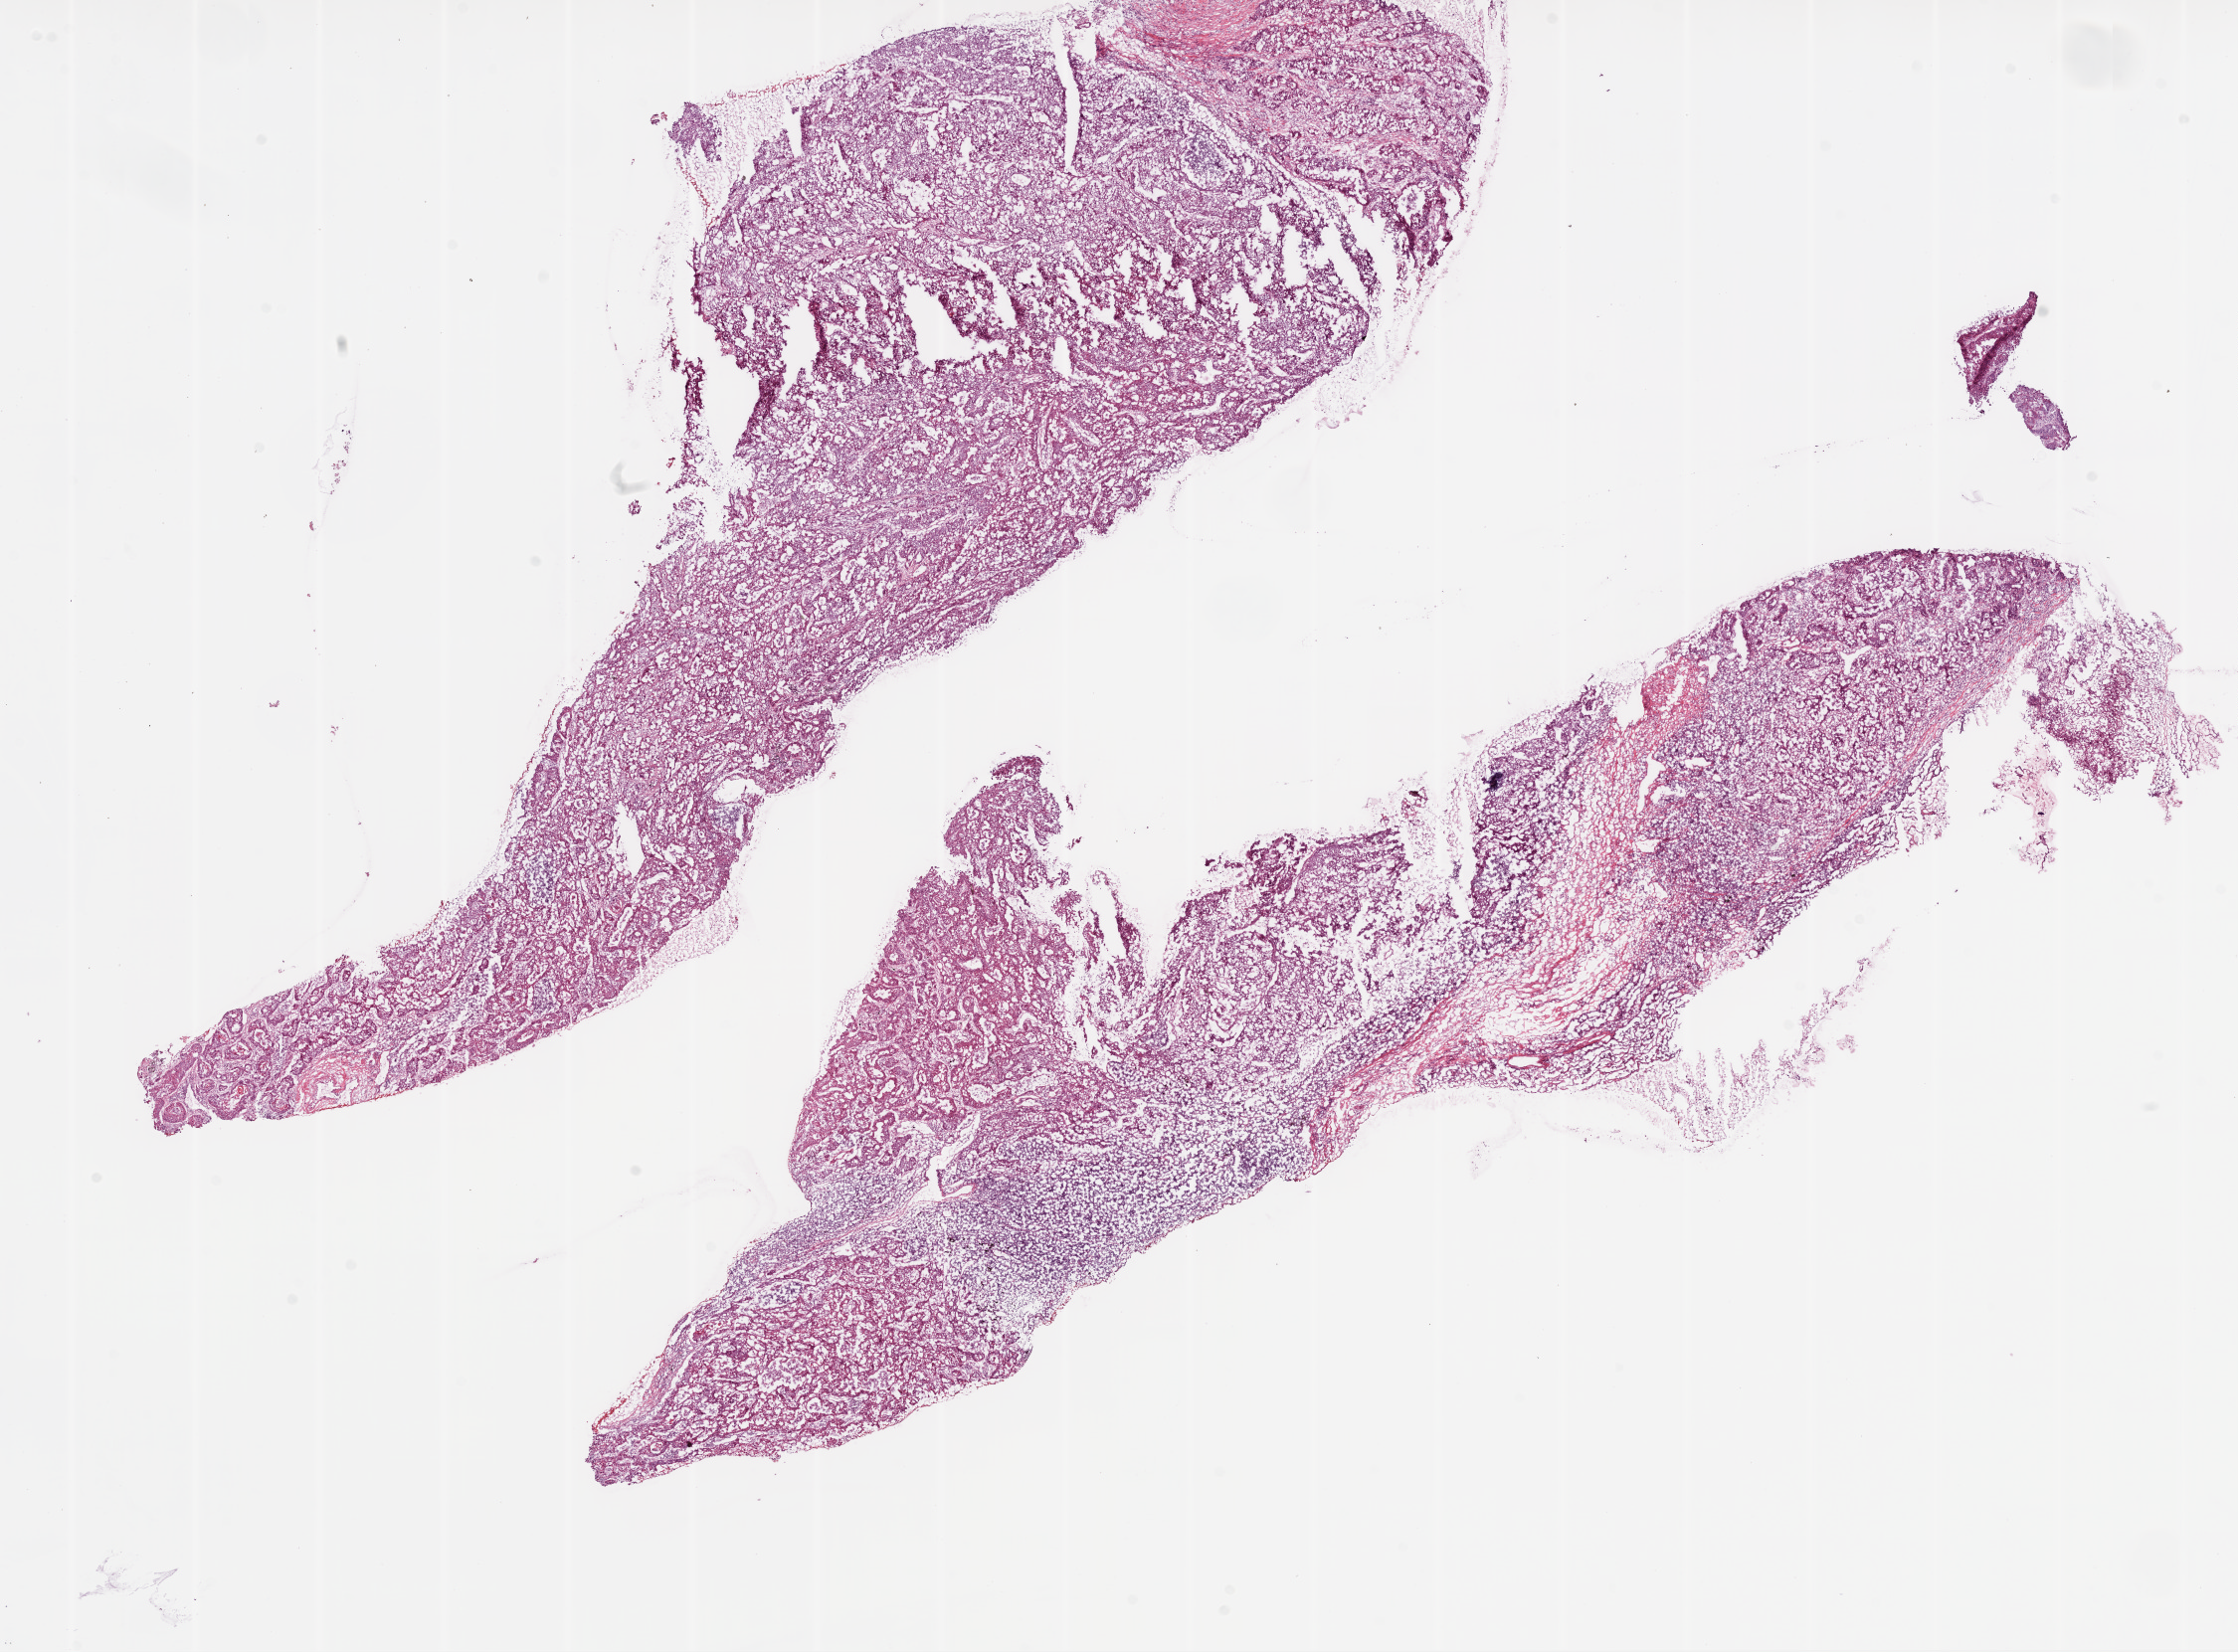
H&E-stained whole-slide image, a low-resolution overview of the entire scanned area, about 18.1 x 13.3 mm, frozen section, primary tumour sample from the lung. Male, age 44 years at initial diagnosis. Slide review estimates, as recorded: tumour cells 80%, tumour nuclei 70%, normal cells 0%, stromal cells 15%, necrosis 5%. Infiltration values recorded for this section: lymphocyte infiltration 15%, monocyte infiltration 2%, neutrophil infiltration 2%.
Pathologic diagnosis: Basaloid squamous cell carcinoma (lower lobe, lung). AJCC pathologic stage: IIA (6th edition). TNM: T2a N1 M0.